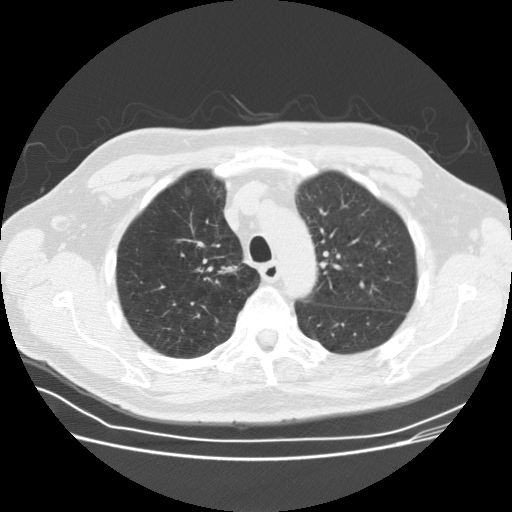
Low-dose screening chest CT, one axial slice; slice 121 of 164 in the series (ordered by position); reconstruction kernel STANDARD; lung window (W 1500 / L -600 HU); 2.5 mm slice thickness; 512 × 512 image matrix, field of view 360 × 360 mm.
Annotated regions visible in this slice (manually delineated by an expert):
- lesion 1 (tumor, upper lobe of right lung): bounding box [x1, y1, x2, y2] px = [218, 264, 238, 274]